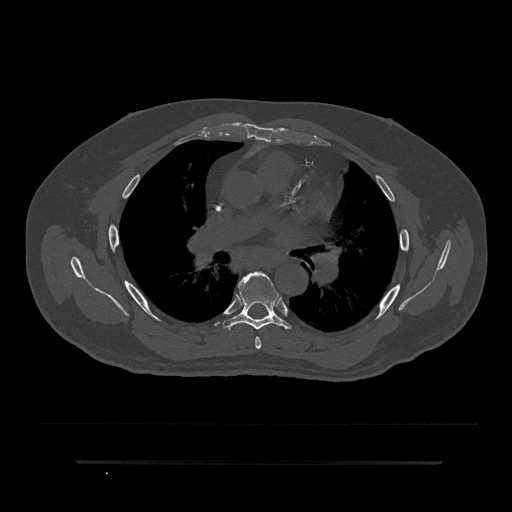
CT including the spine, one axial slice. Position 535 of 797 along the scan axis. Reconstruction kernel Br40s/3. 120 kVp. Bone window (W 1800 / L 400 HU). 512 × 512 image matrix. Male patient, age 59 years. From the clinical record (not read from this slice): primary cancer: bile ducts.
Structures marked on this image (semi-automatically segmented with operator editing):
- T5 vertebra: bounding box <255,337,262,349> (left, top, right, bottom; pixels)
- T6 vertebra: <222,271,291,330>